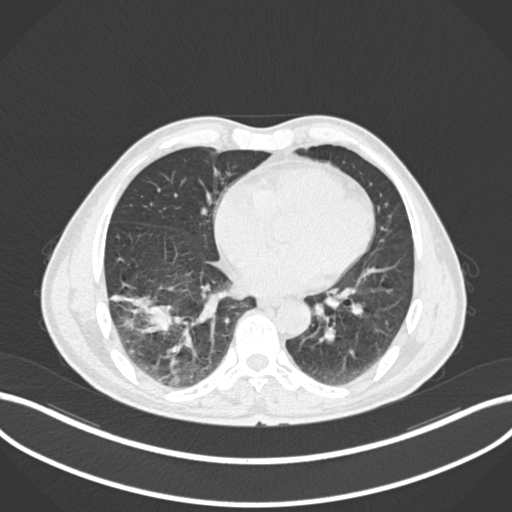
Chest CT, one axial slice. Reconstruction kernel B30f. Lung window (W 1500 / L -600 HU). 512 × 512 image matrix, field of view 400 × 400 mm. Patient: male, 58 years. From the clinical record (not read from this slice): clinical TNM (as recorded): T3 N0 M0; histopathological grade: G2.
Annotated regions visible in this slice (bounding box drawn by a radiologist):
- lung tumour (recorded histology: squamous cell carcinoma): bounding box [x1, y1, x2, y2] px = [104, 286, 180, 337]